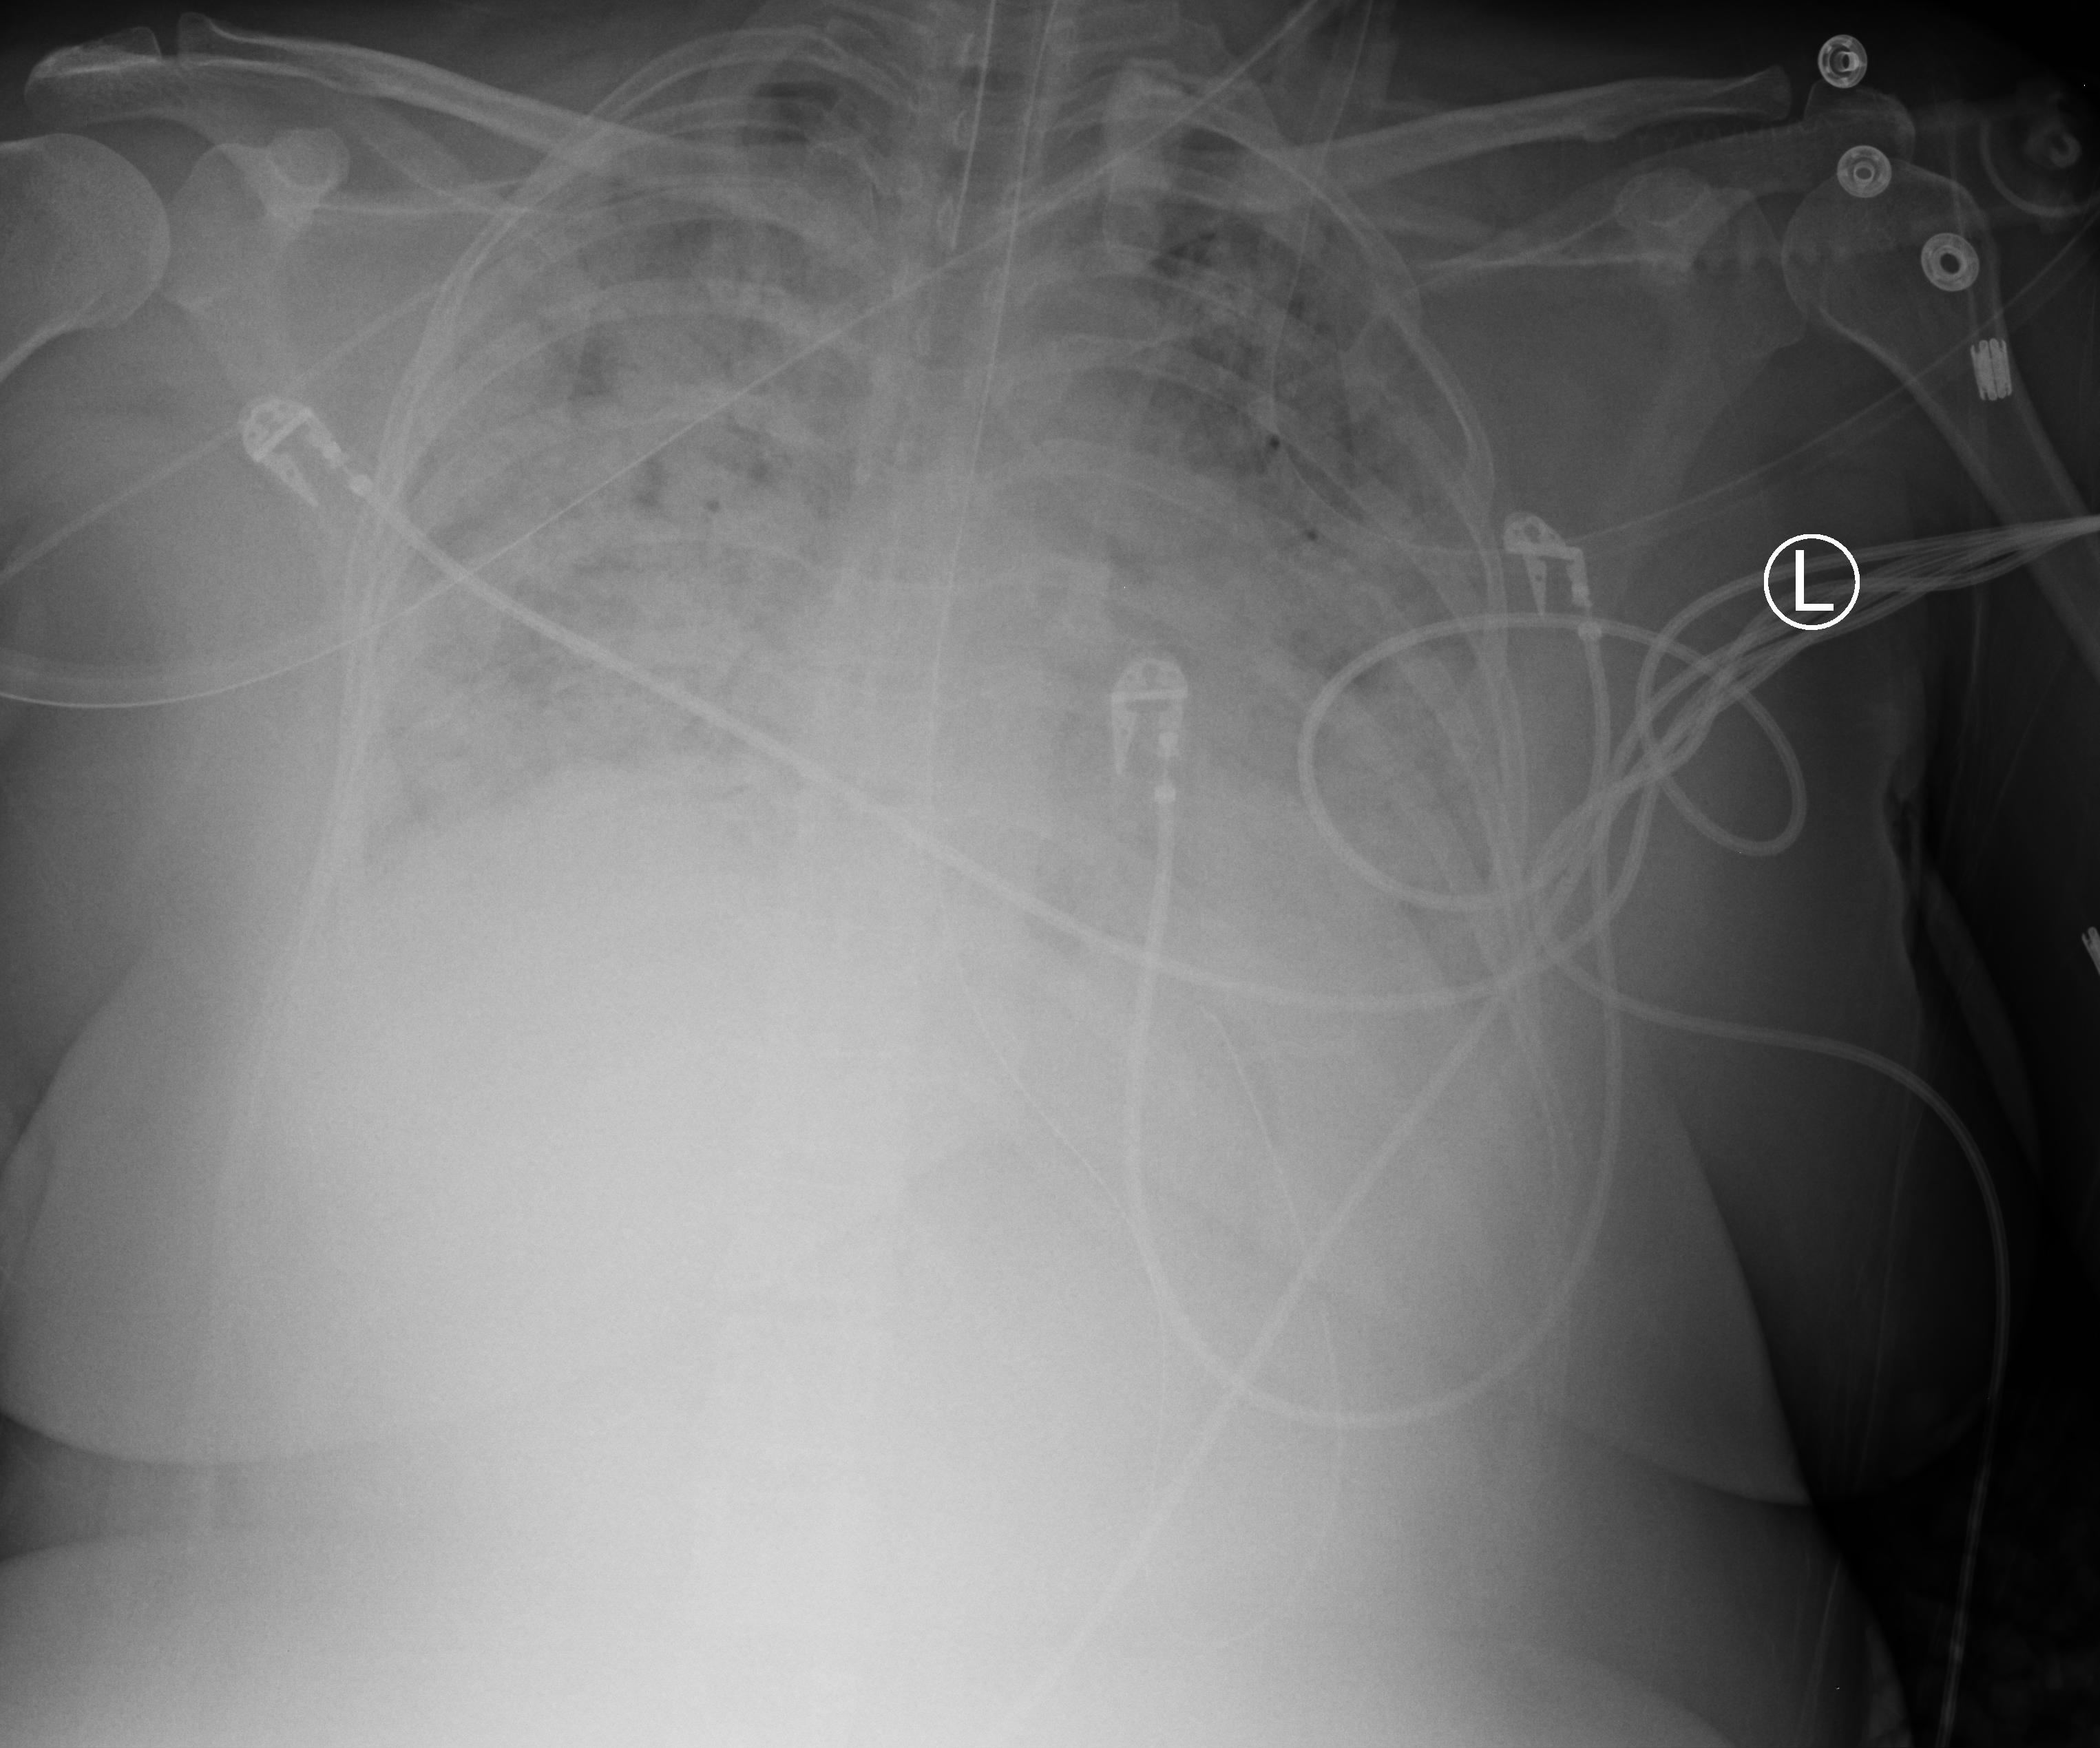
Bedside chest radiograph (computed radiography). Adult patient hospitalised with COVID-19, age 18–59 years.
From the hospital-stay record, not from the radiograph (when in the stay this image was taken is not recorded): chronic kidney disease (admission record): no.